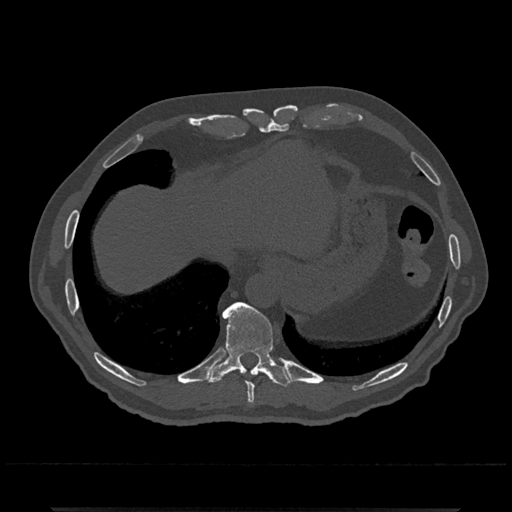
CT including the spine, one axial slice; position 571 of 797 along the scan axis; reconstruction kernel Br40s/3; 120 kVp; bone window (W 1800 / L 400 HU); 0.5 mm slice thickness; 512 × 512 image matrix, field of view 393 × 393 mm. Male patient, age 67 years. Case-level facts recorded for this patient, not image findings: primary cancer: prostate.
Annotated regions visible in this slice (semi-automatically segmented with operator editing):
- T10 vertebra: bounding box [x1, y1, x2, y2] px = [207, 302, 291, 387]
- T9 vertebra: [247, 382, 255, 404]